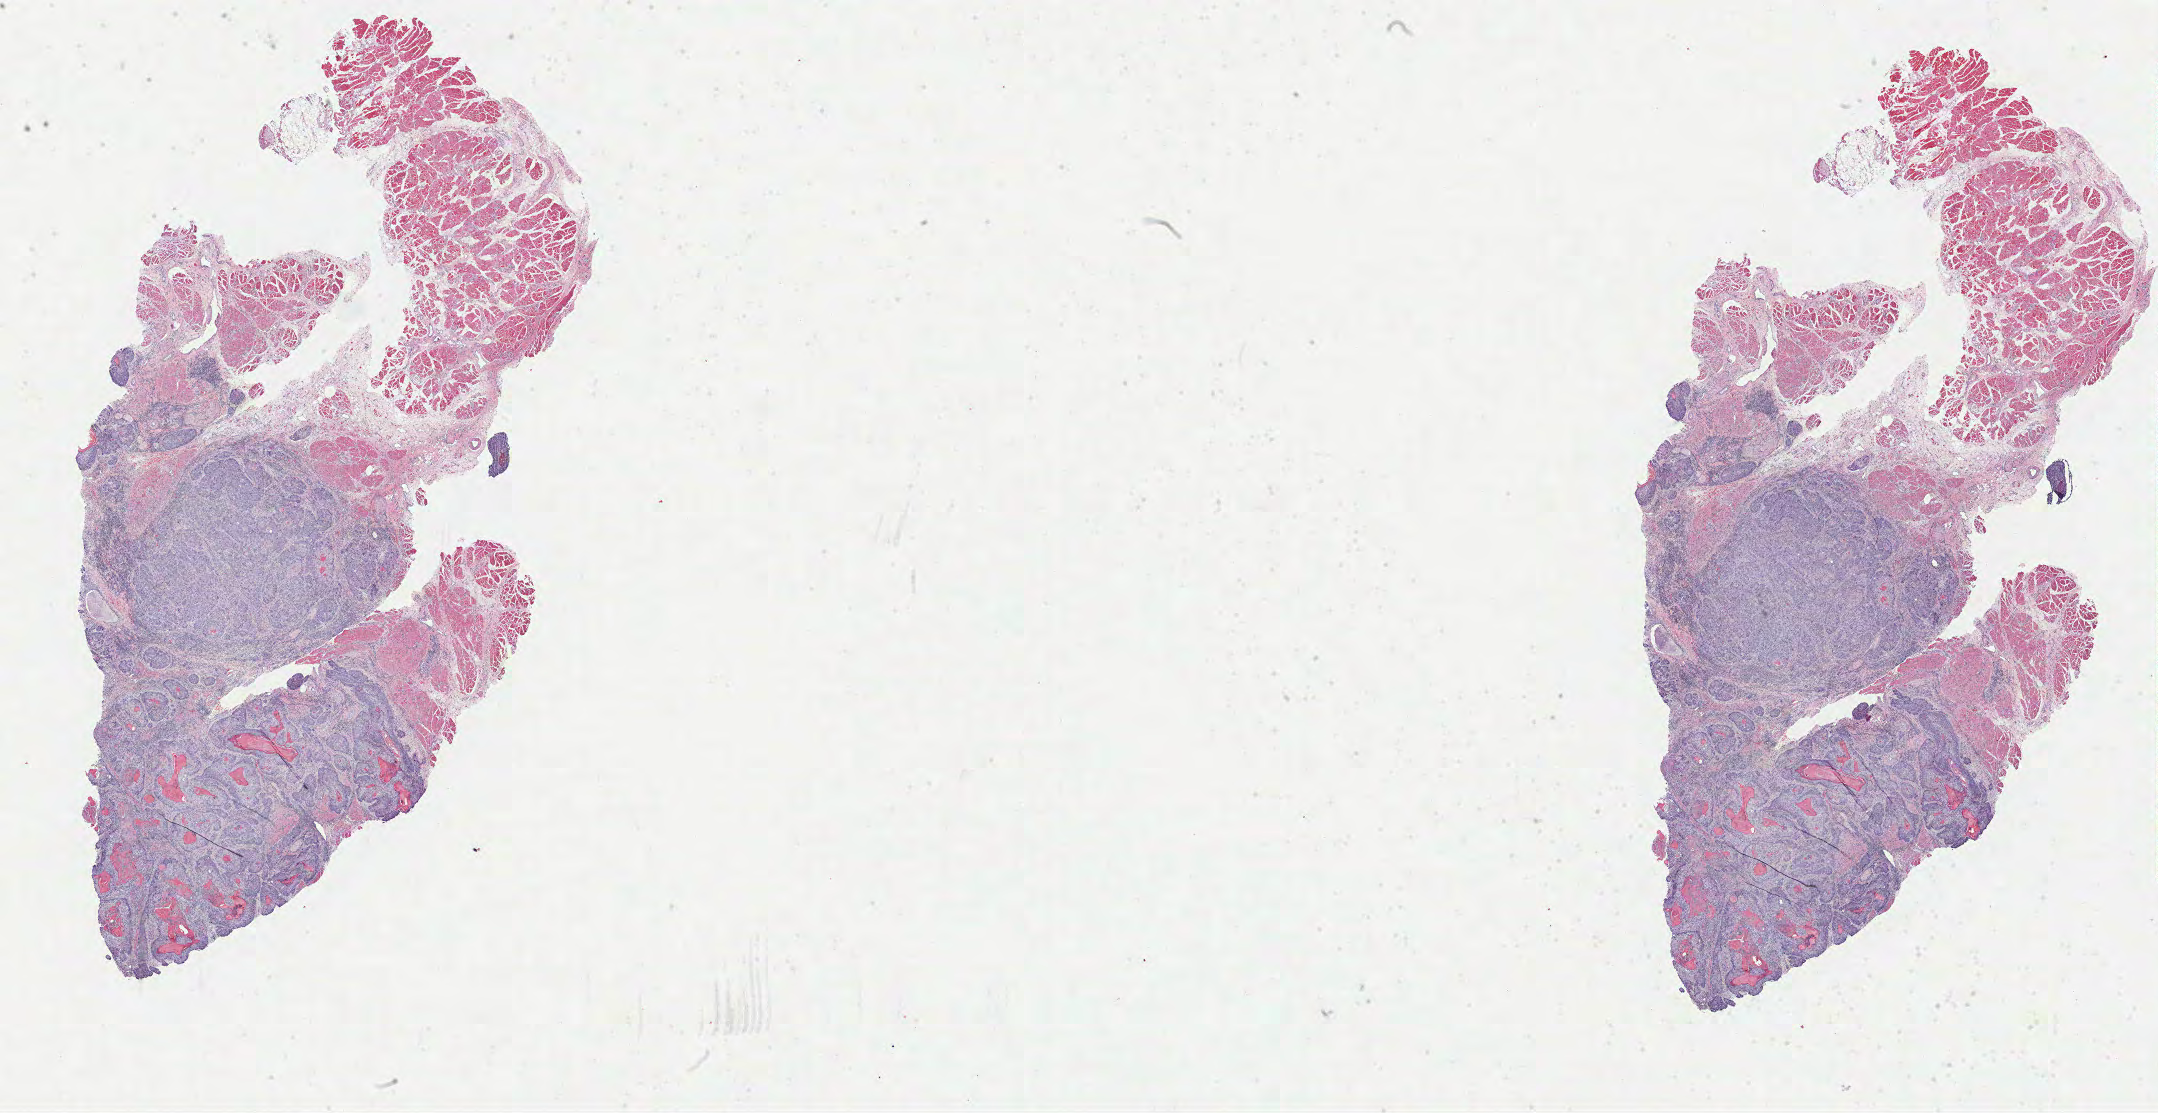
Digitized Hematoxylin and eosin (H&E) stained tissue section (whole slide) — a low-resolution overview of the entire scanned area, about 34.8 x 18.0 mm (slide scanned at 40x). Formalin-fixed paraffin-embedded (FFPE) diagnostic section. Sample: primary tumour, head and neck. Male patient; age at initial diagnosis 59 years. Histologic grade: G2 (moderately differentiated).
• histologic diagnosis: Squamous cell carcinoma, NOS (floor of mouth, NOS)
• AJCC pathologic stage: IVA
• TNM: T4a N2b M0